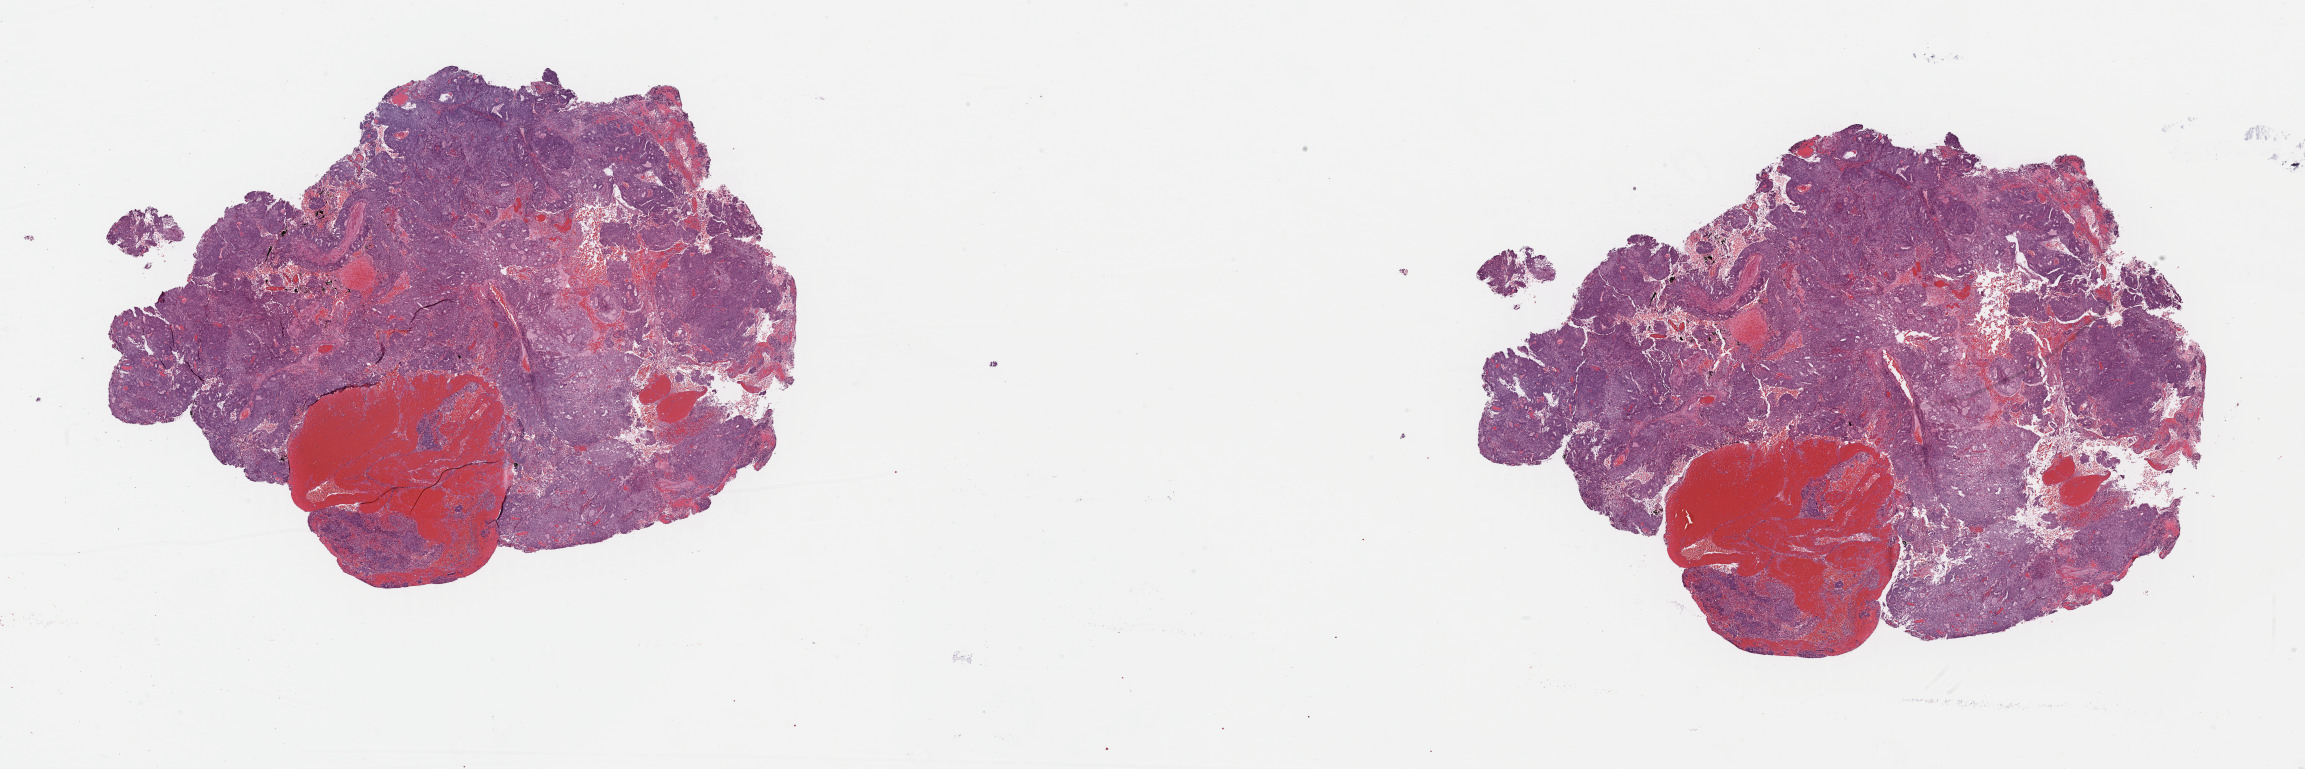
Whole-slide histology image, H&E, a low-resolution overview of the entire scanned area, about 36.4 x 12.1 mm (from a 40x scan); FFPE section; sample: primary tumour, uterus. Female, age 58 years at initial diagnosis. Histologic grade: G3 (poorly differentiated).
- FIGO stage: IB
- pathologic diagnosis: Endometrioid adenocarcinoma, NOS (endometrium)